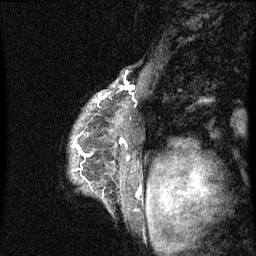
Breast MRI (dynamic contrast-enhanced), one sagittal slice; slice 53 of 60 in the series (ordered by position); dynamic contrast-enhanced series, image 2 of 3 at this slice position (ordered by acquisition); 1.5 T; TE 4.2 ms, TR 8 ms; 2 mm slice thickness; 256 × 256 image matrix, field of view 190 × 190 mm. Female patient, age 50 years.
Annotated regions visible in this slice (semi-automatically segmented with operator editing):
- analysis volume of interest (the breast-tissue region the enhancement analysis was run in; not a lesion): bounding box (x1, y1, x2, y2) in pixels: (71, 92, 142, 212)
- tumour enhancement mask (voxels above the 70 % enhancement threshold inside the analysis volume of interest): (73, 100, 97, 149)